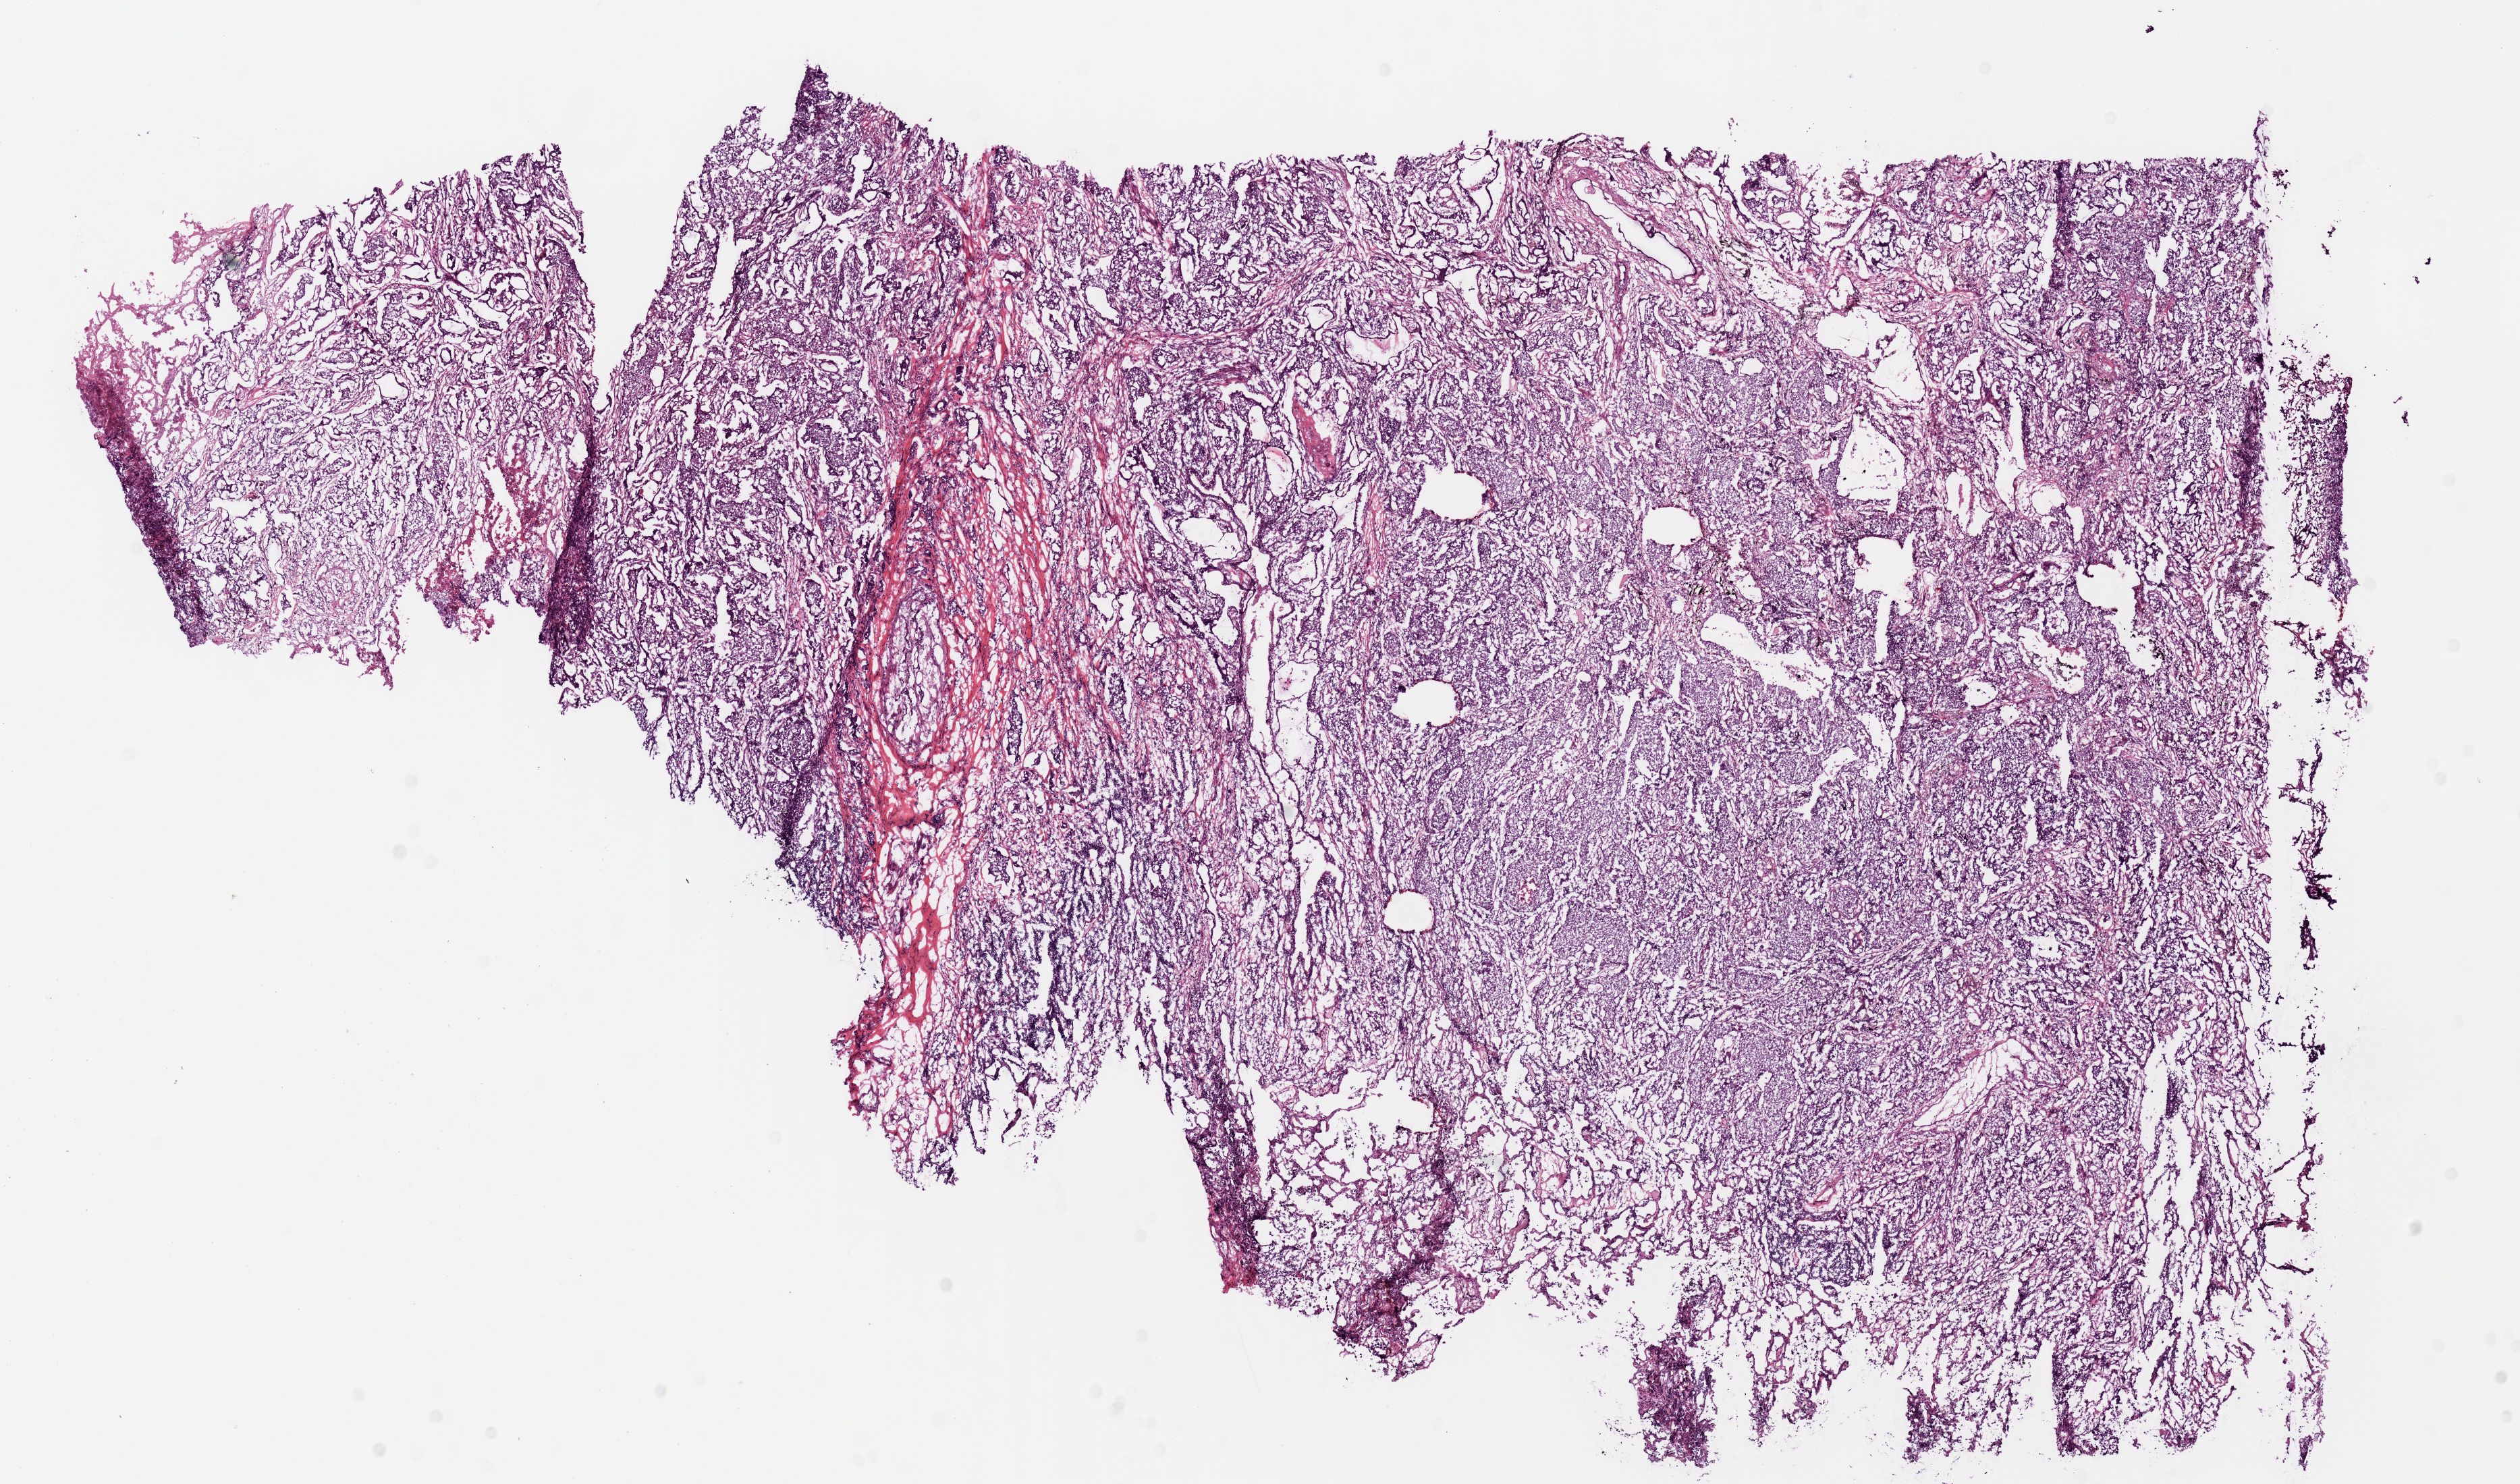
Digitized H&E tissue section (whole slide), shown as a low-resolution overview of the whole scanned area (about 14.8 x 8.7 mm); frozen section from the top of the tissue portion; sample: primary tumour, lung. Patient: male, age at initial diagnosis 71 years. Slide review estimates, as recorded: tumour nuclei 75%, necrosis 5%.
TNM: T2a N1 M0. AJCC pathologic stage: IIA. Pathologic diagnosis: Papillary squamous cell carcinoma.